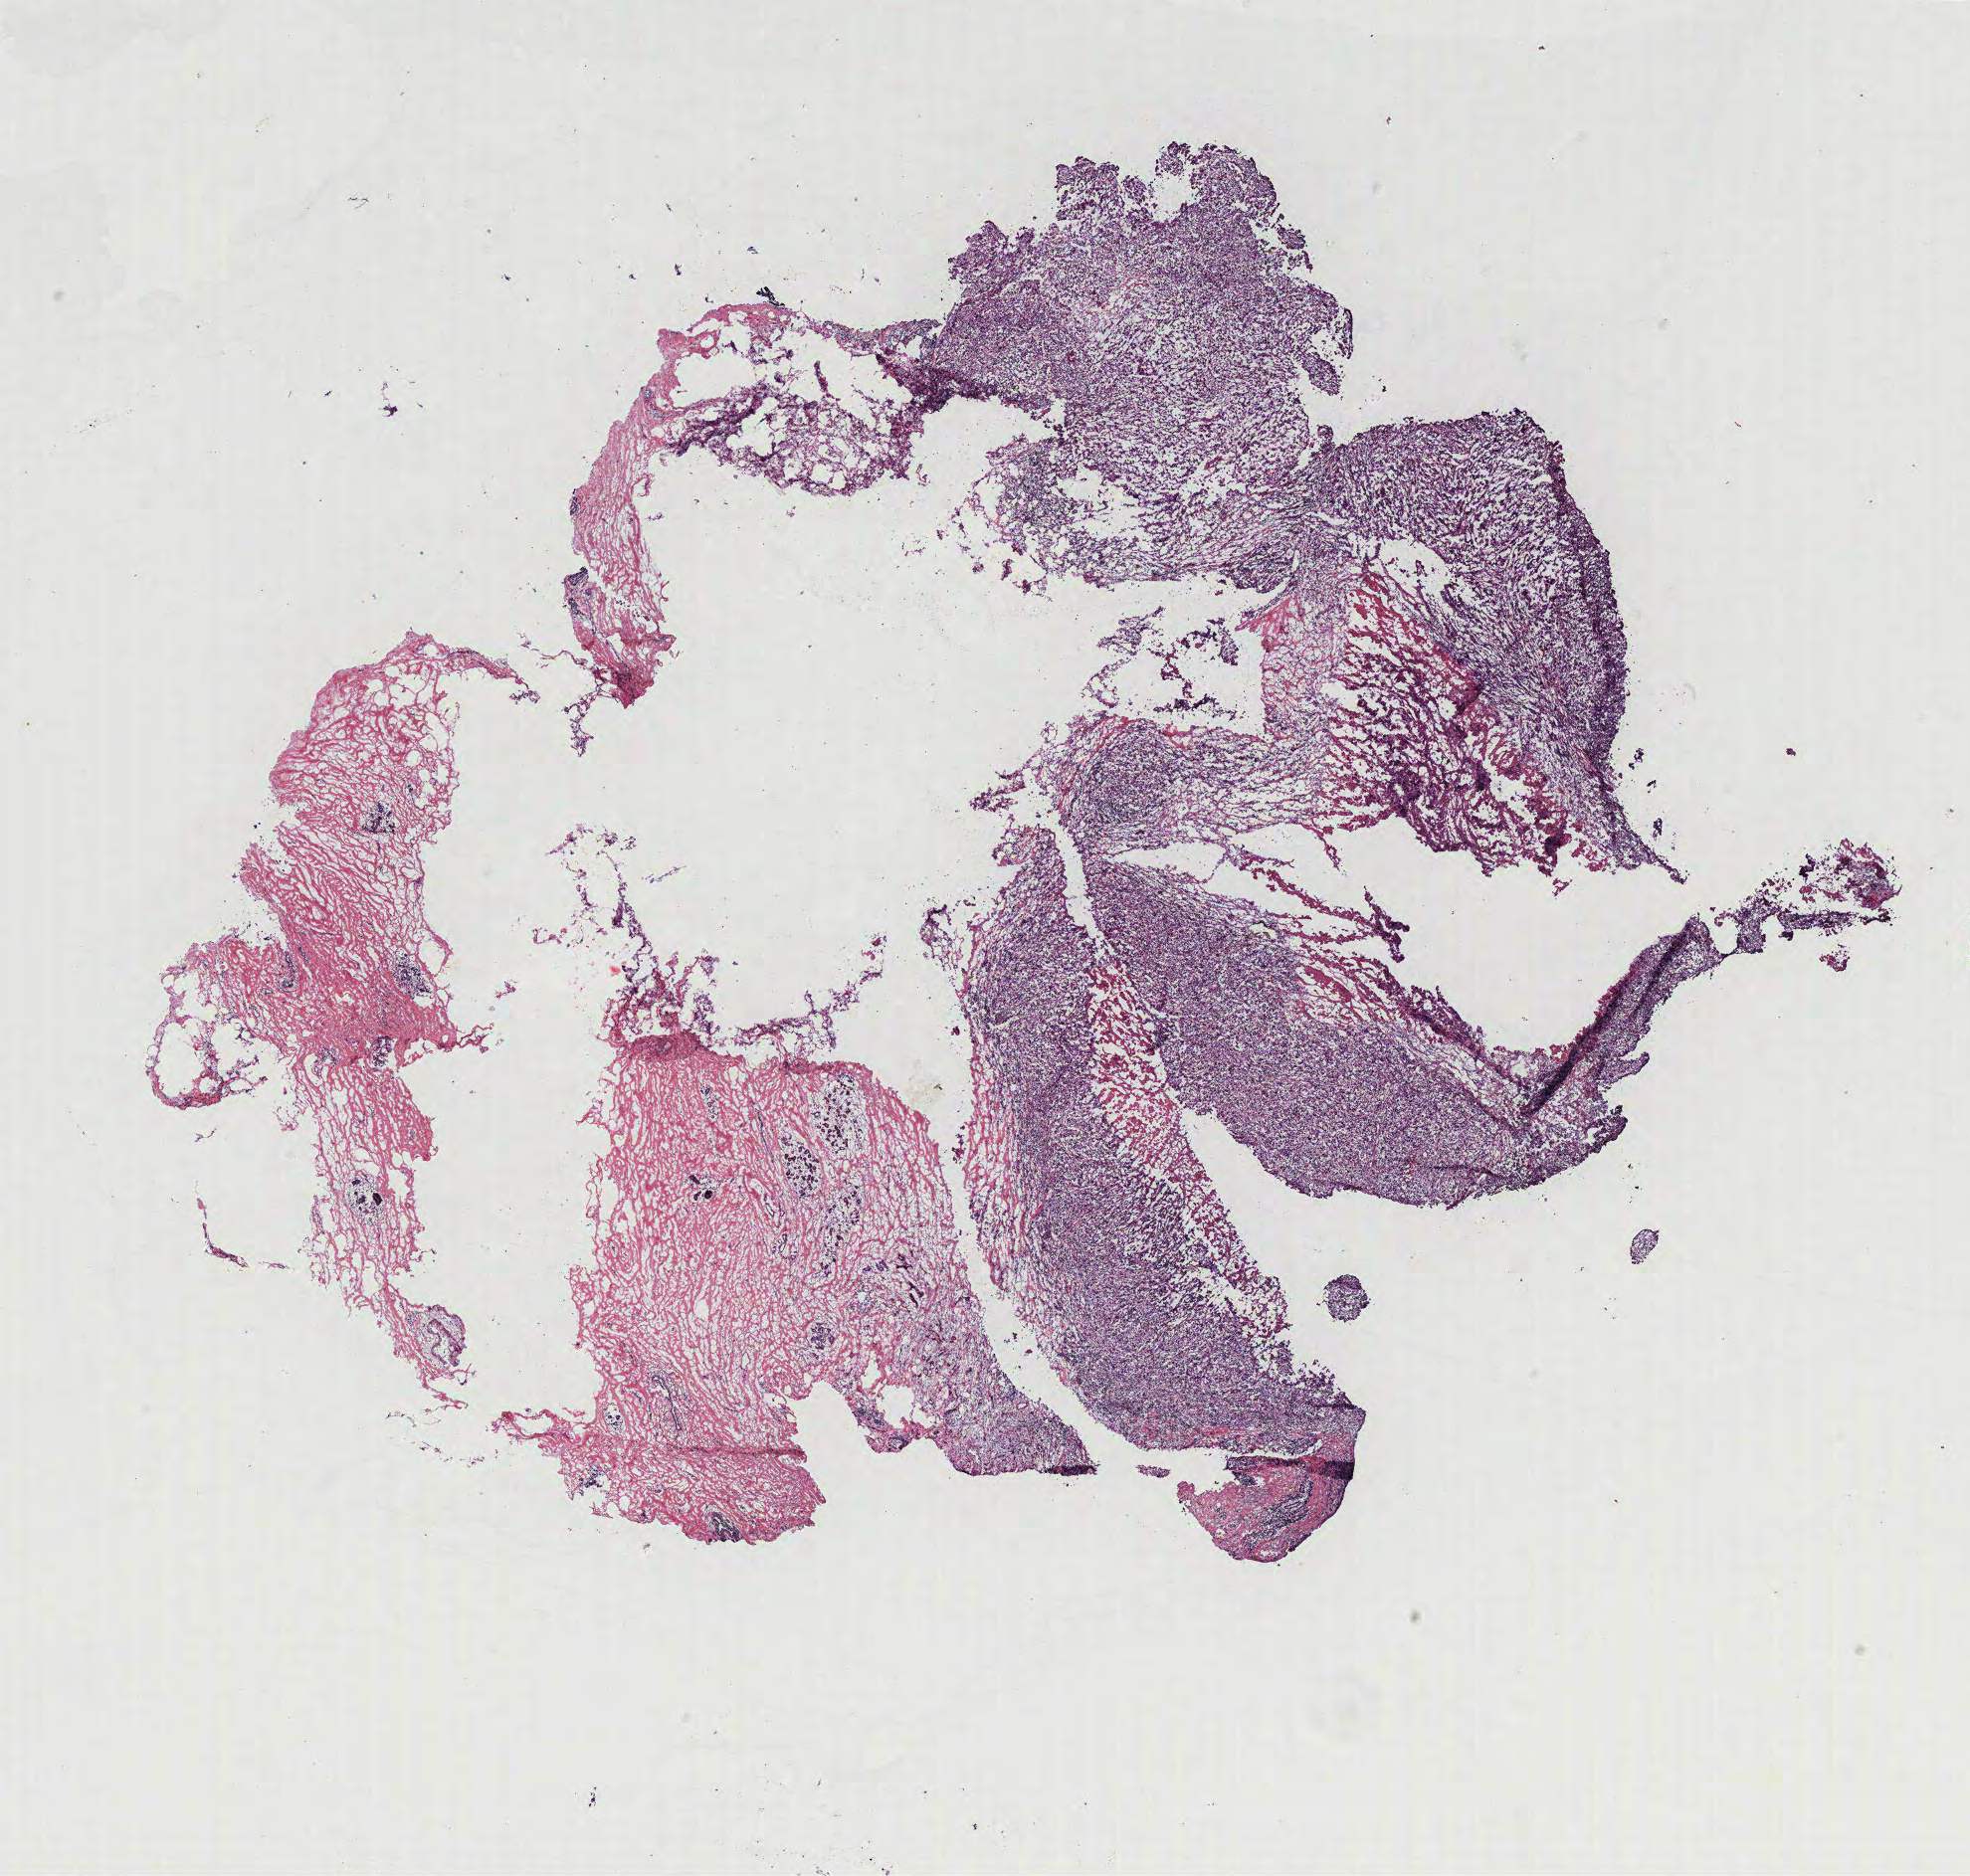
H&E-stained whole-slide image — a low-resolution overview of the entire scanned area, about 15.8 x 15.1 mm (from a 40x scan), breast, tissue type not recorded.
- patient diagnosis (cohort enrolment): breast cancer (breast)